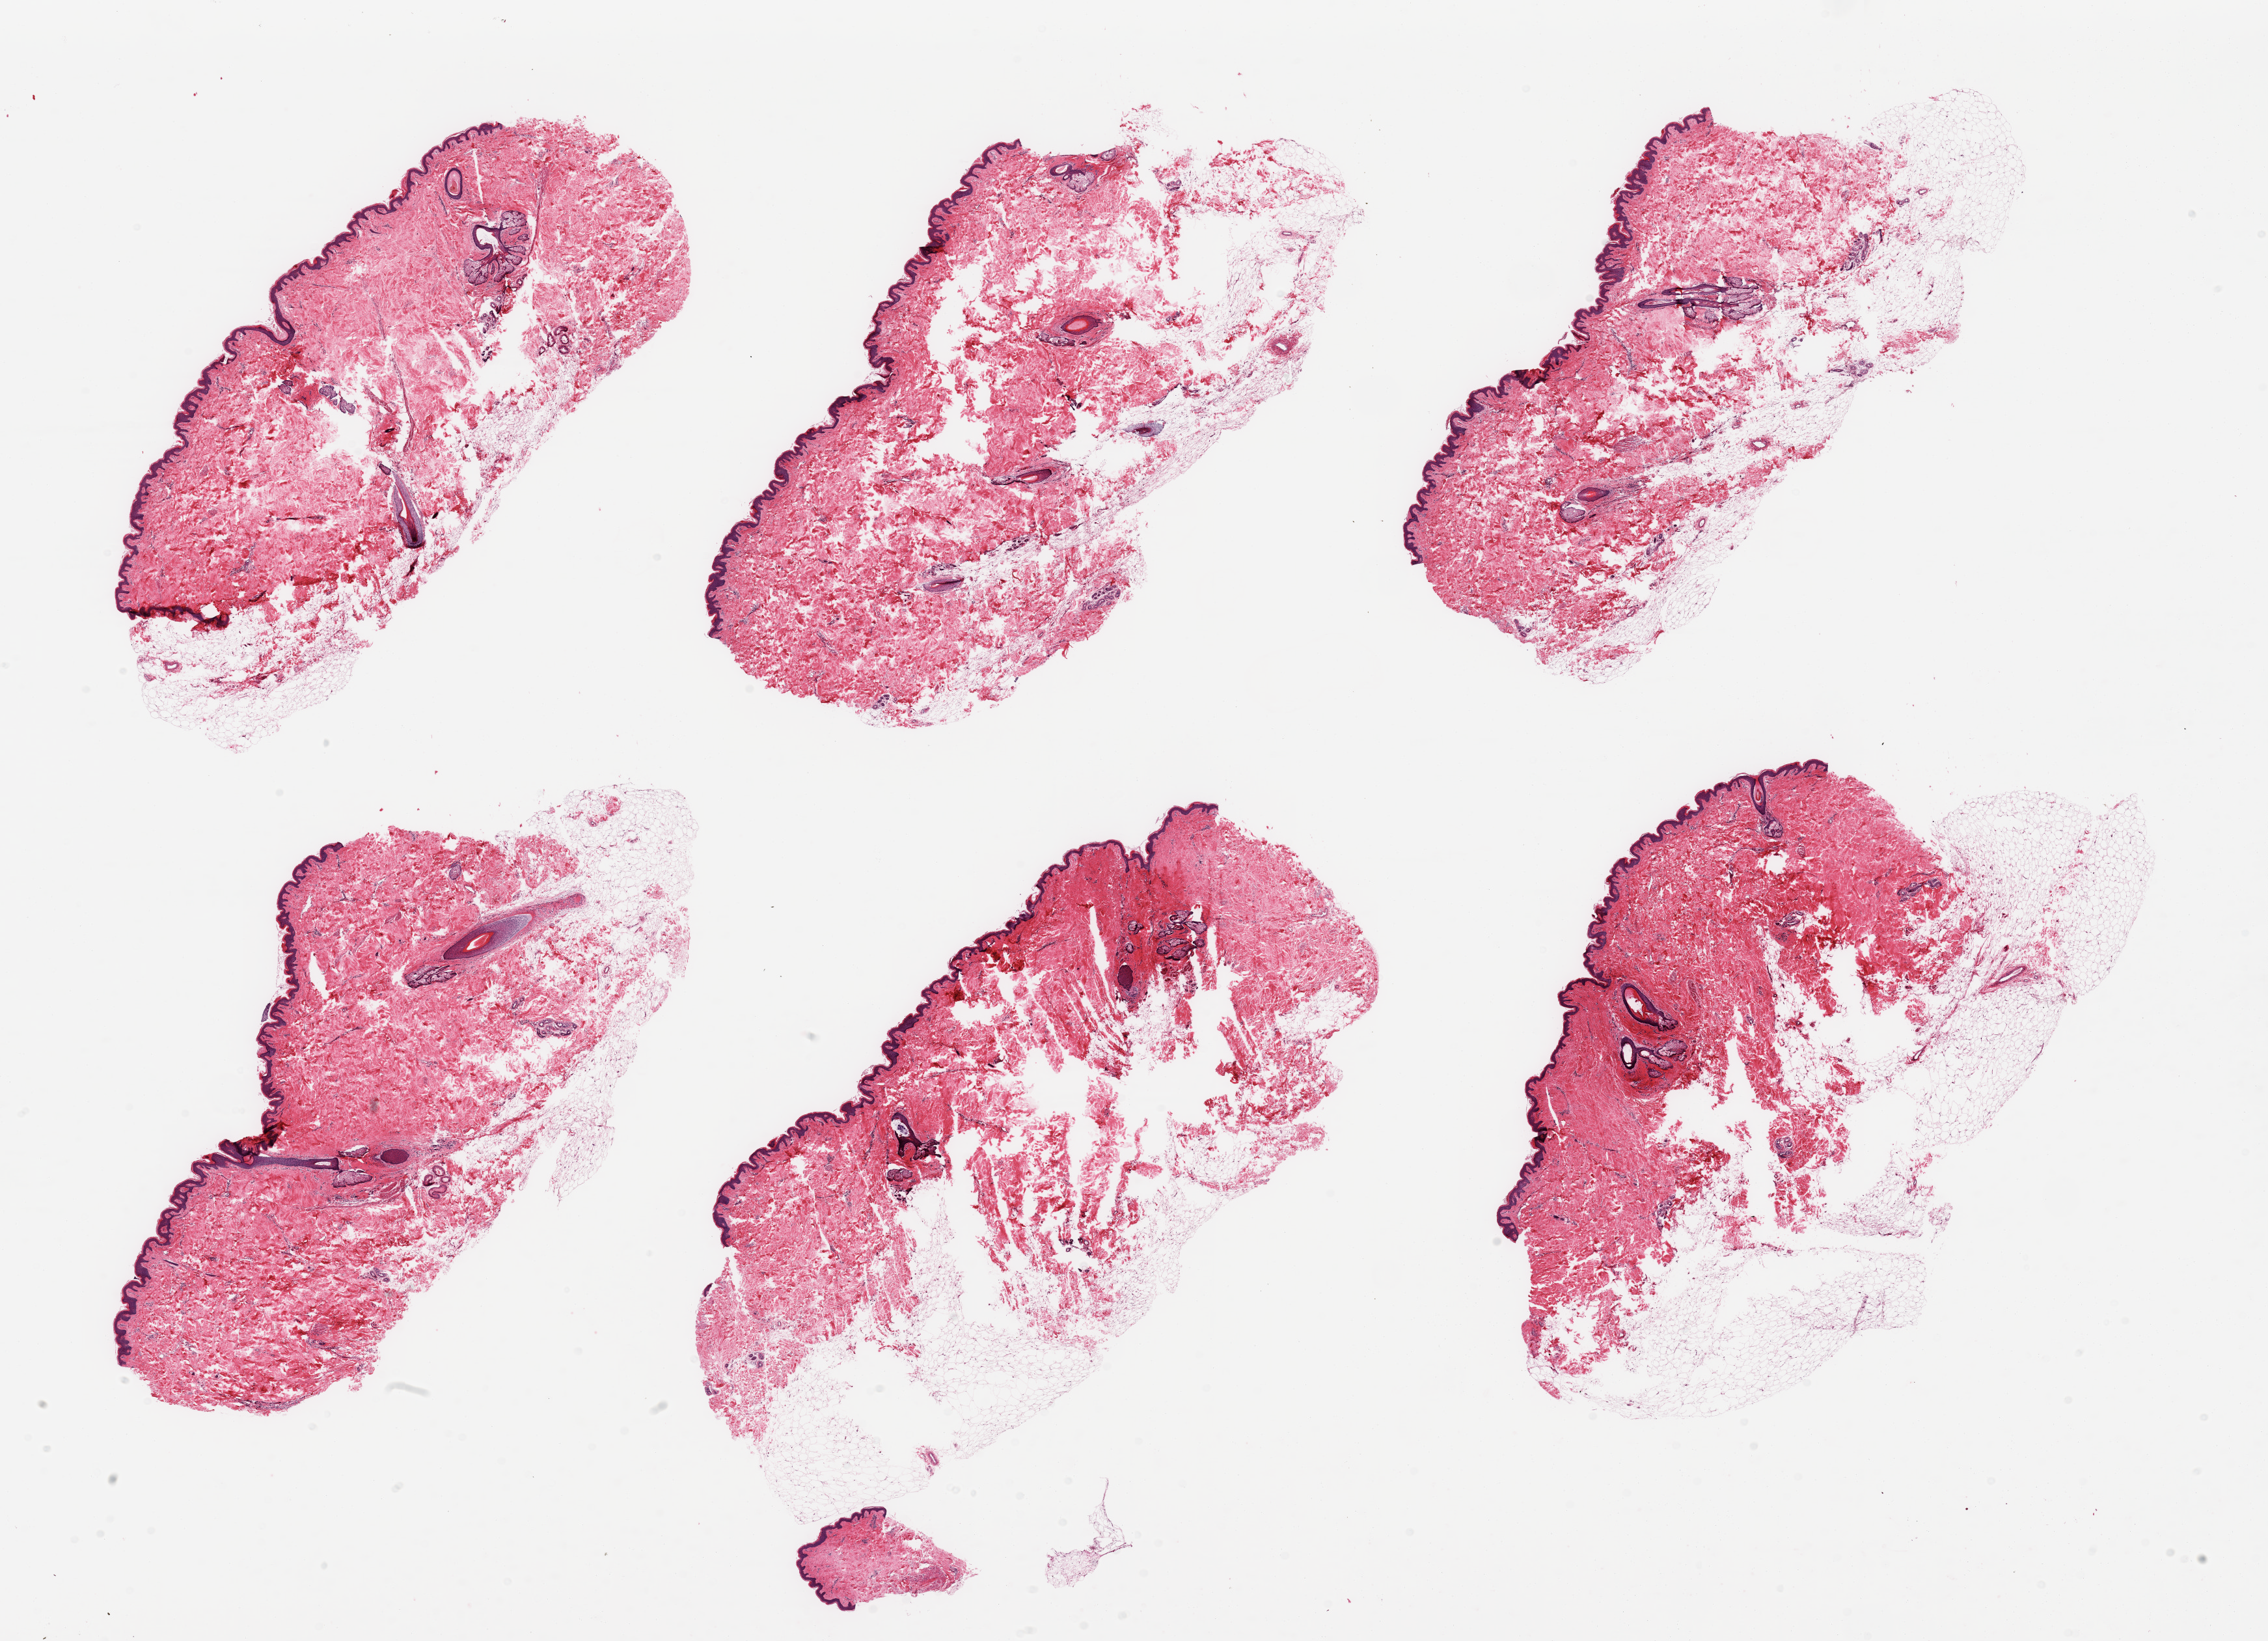
Digitized haematoxylin and eosin-stained section, whole scanned area (about 27.6 x 19.9 mm) shown as a low-resolution overview. PAXgene-fixed paraffin-embedded (PFPE) section. Target tissue: skin of suprapubic region. Tissue donor sample. Donor: female.
- review note (as recorded): 6 pieces; hair bearing skin with mild to moderate autolysis; 20% to 50% external fat